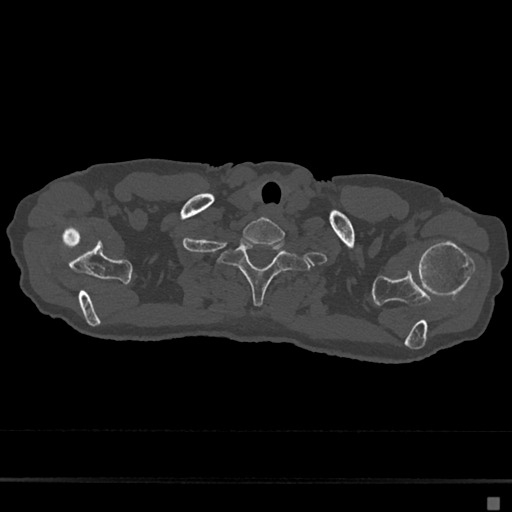
CT including the spine, one axial slice; position 613 of 797 along the scan axis; bone window (W 1800 / L 400 HU); 0.5 mm slice thickness; 512 × 512 image matrix. Patient: female, 68 years. From the clinical record (not read from this slice): primary cancer: renal.
Outlined on this slice (semi-automatic segmentation, software-assisted and operator-edited):
- T1 vertebra: bounding box (x1, y1, x2, y2) in pixels: (218, 238, 311, 306)